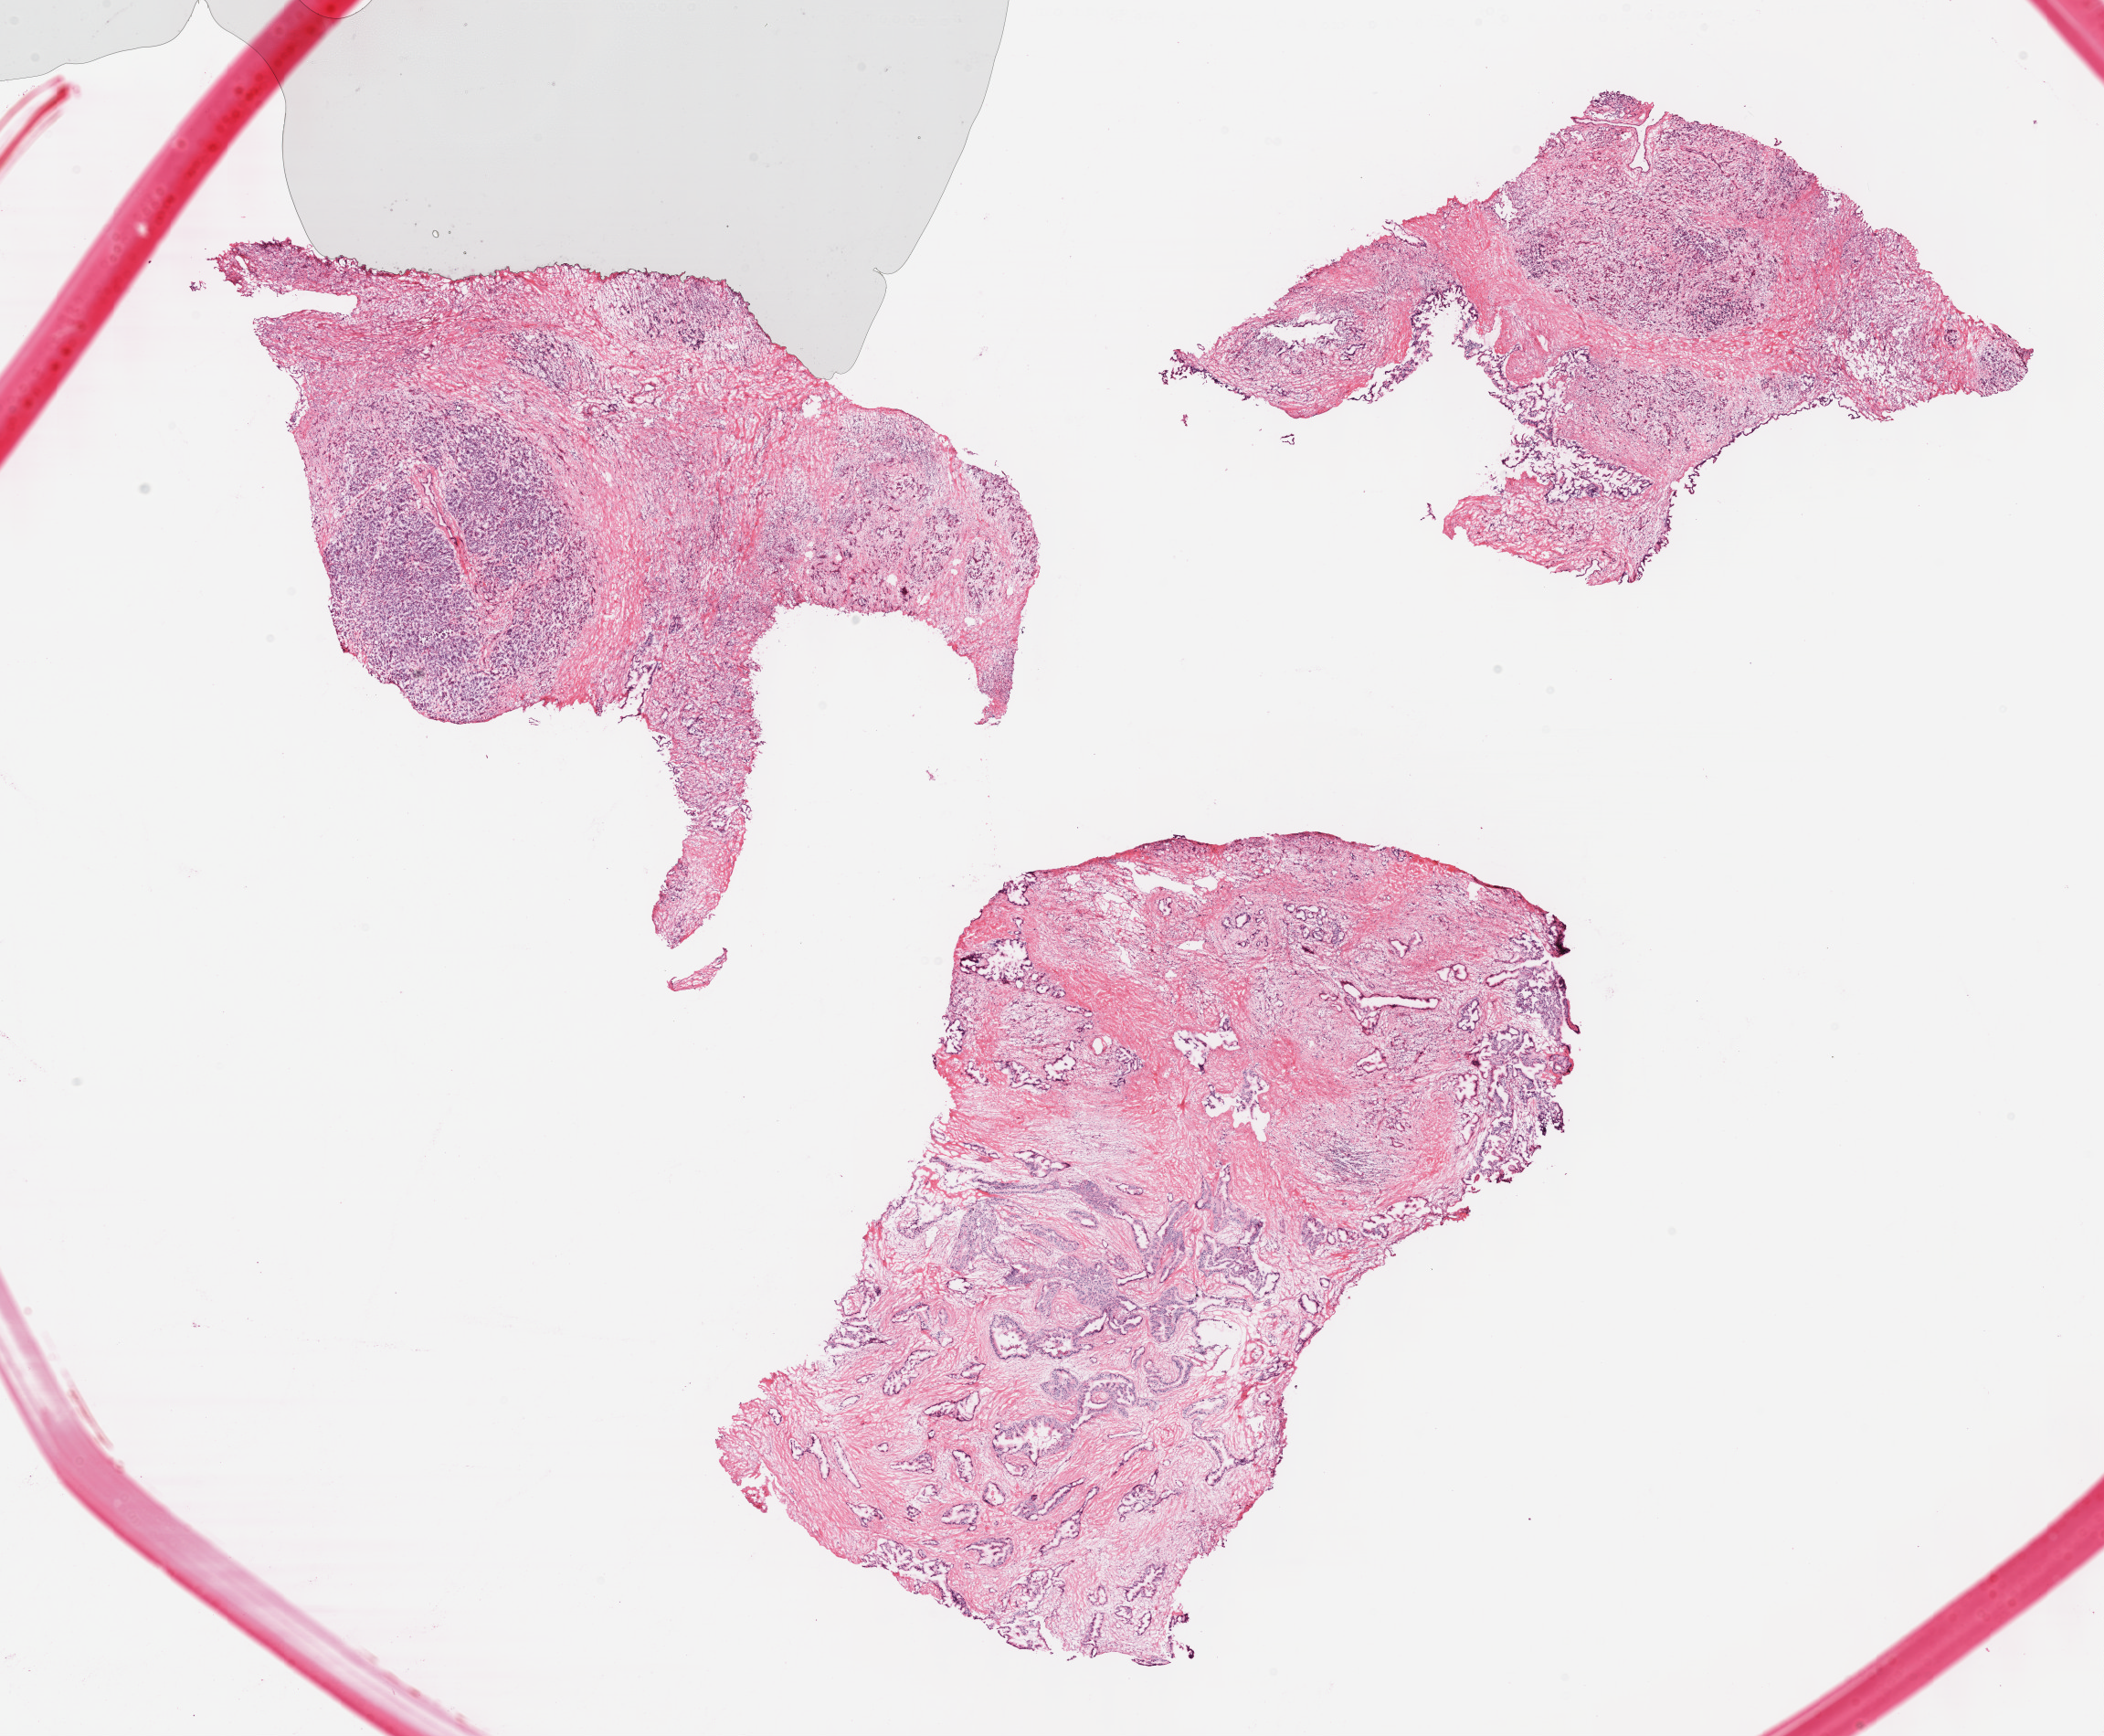
Whole-slide histology image, Hematoxylin and eosin (H&E) stained — shown as a low-resolution overview of the whole scanned area (about 18.6 x 15.4 mm, acquisition: 40x scan). Formalin-fixed paraffin-embedded (FFPE) diagnostic section. Pancreas, primary tumour sample. Patient: male, age at initial diagnosis 68 years. Histologic grade: G3 (poorly differentiated).
Lymph nodes positive (case pathology): 0 of 18 examined. Histologic diagnosis: Infiltrating duct carcinoma, NOS (head of pancreas). AJCC pathologic stage: IIA (7th edition).